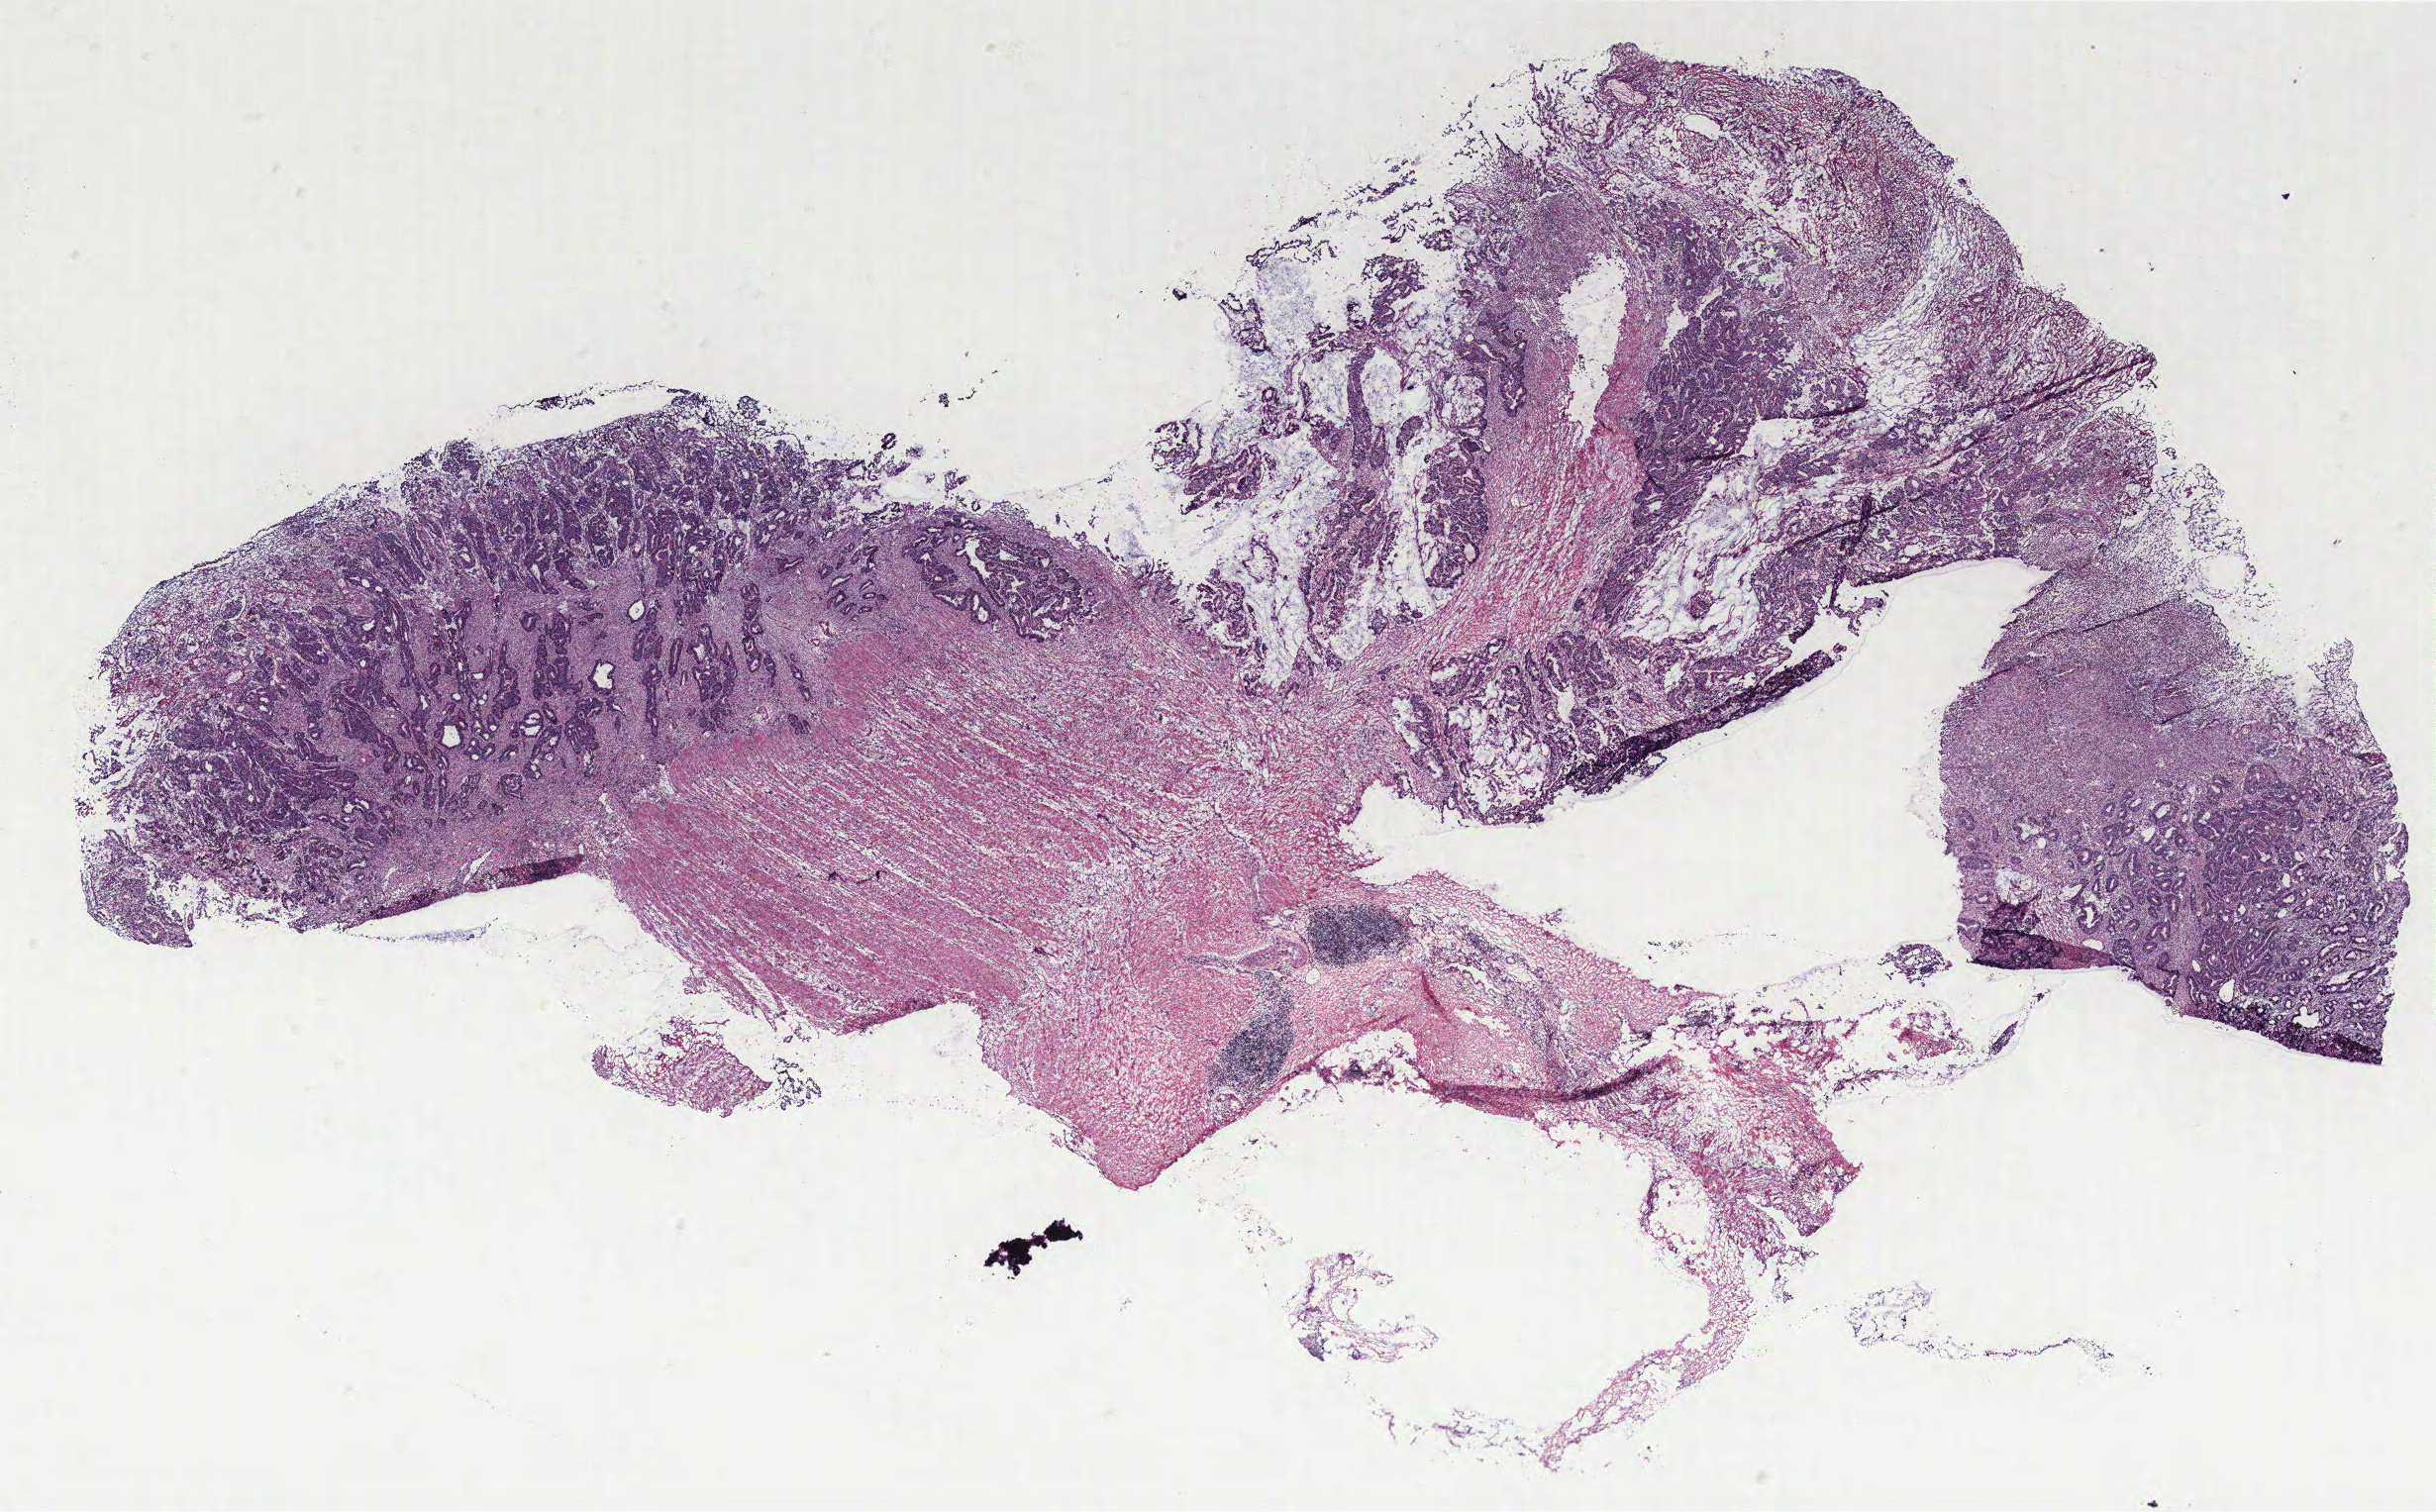
Digitized Hematoxylin and eosin (H&E) stained tissue section (whole slide), shown as a low-resolution overview of the whole scanned area (about 19.7 x 12.2 mm, from a 40x scan), colon, tissue type not recorded. Male patient.
Patient diagnosis: Adenocarcinoma, NOS.